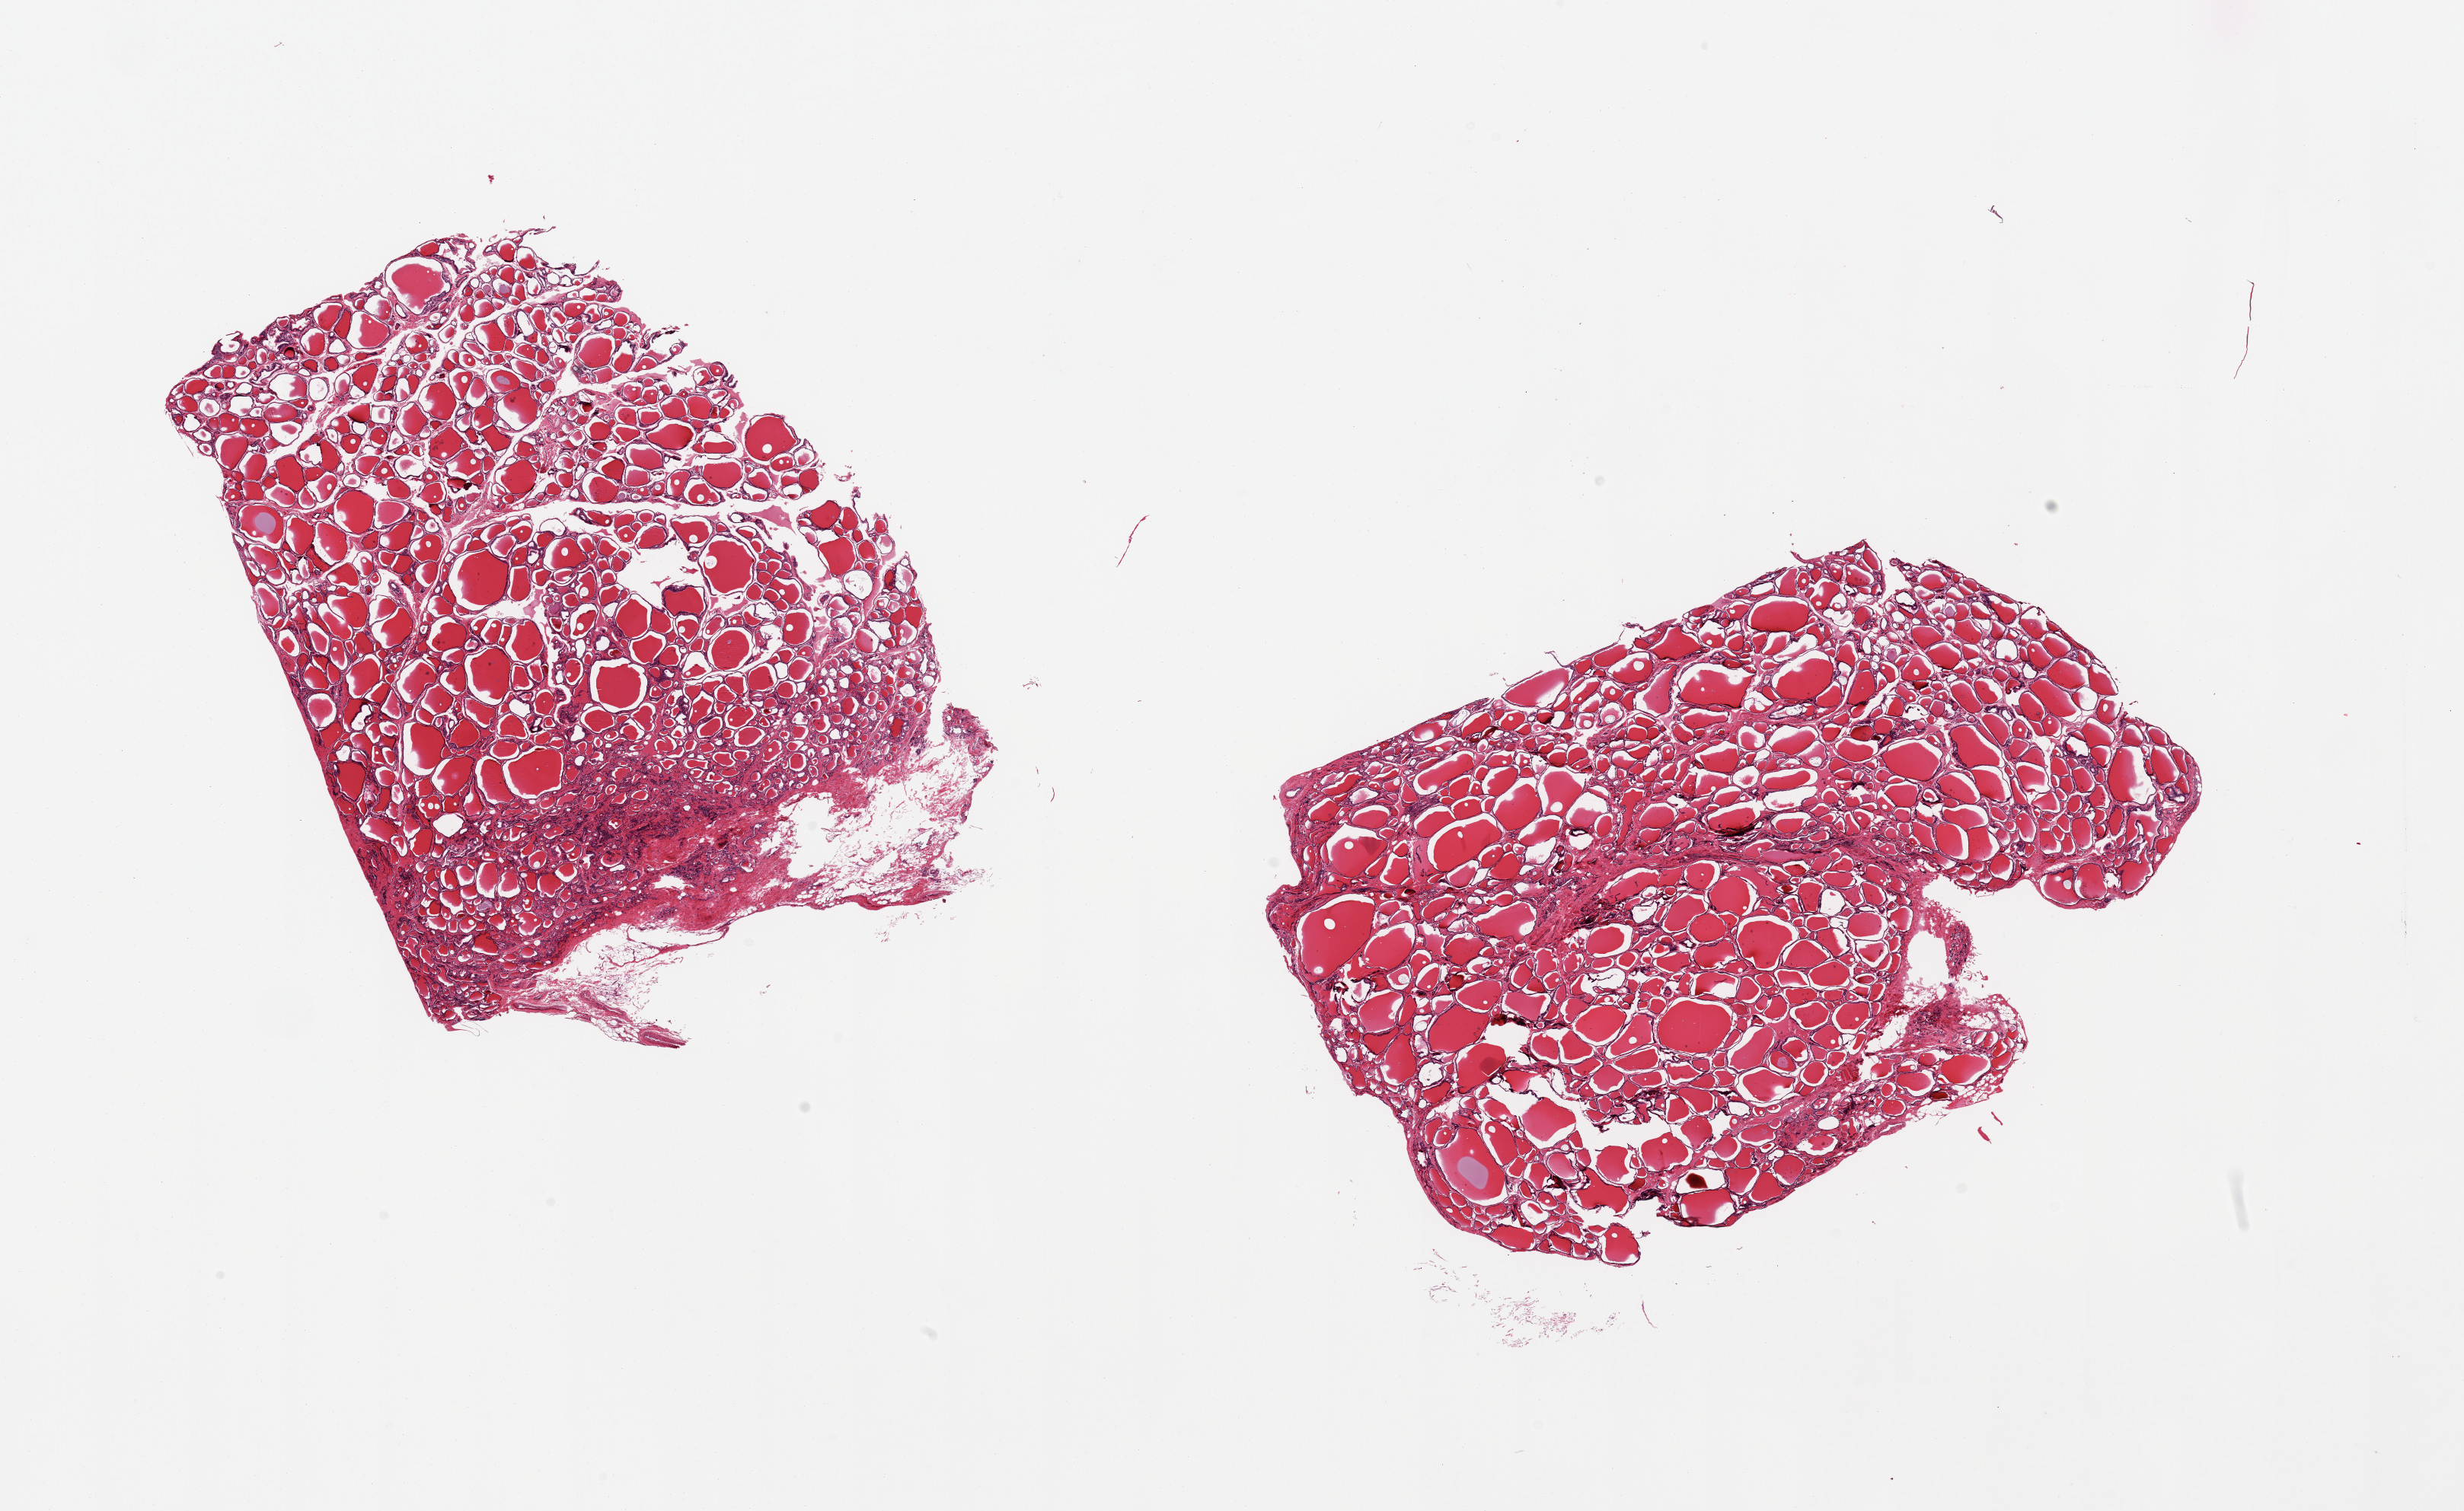
Digitized H&E-stained section — a low-resolution overview of the entire scanned area, about 25.6 x 15.7 mm (from a 20x scan), PAXgene-fixed paraffin-embedded (PFPE) section, target tissue: thyroid, tissue donor sample. Female donor.
• pathologist's review note for this sample: 2 pieces, no abnormalities, one section with nubbin of adherenat fat/vascular elements up to ~1mm